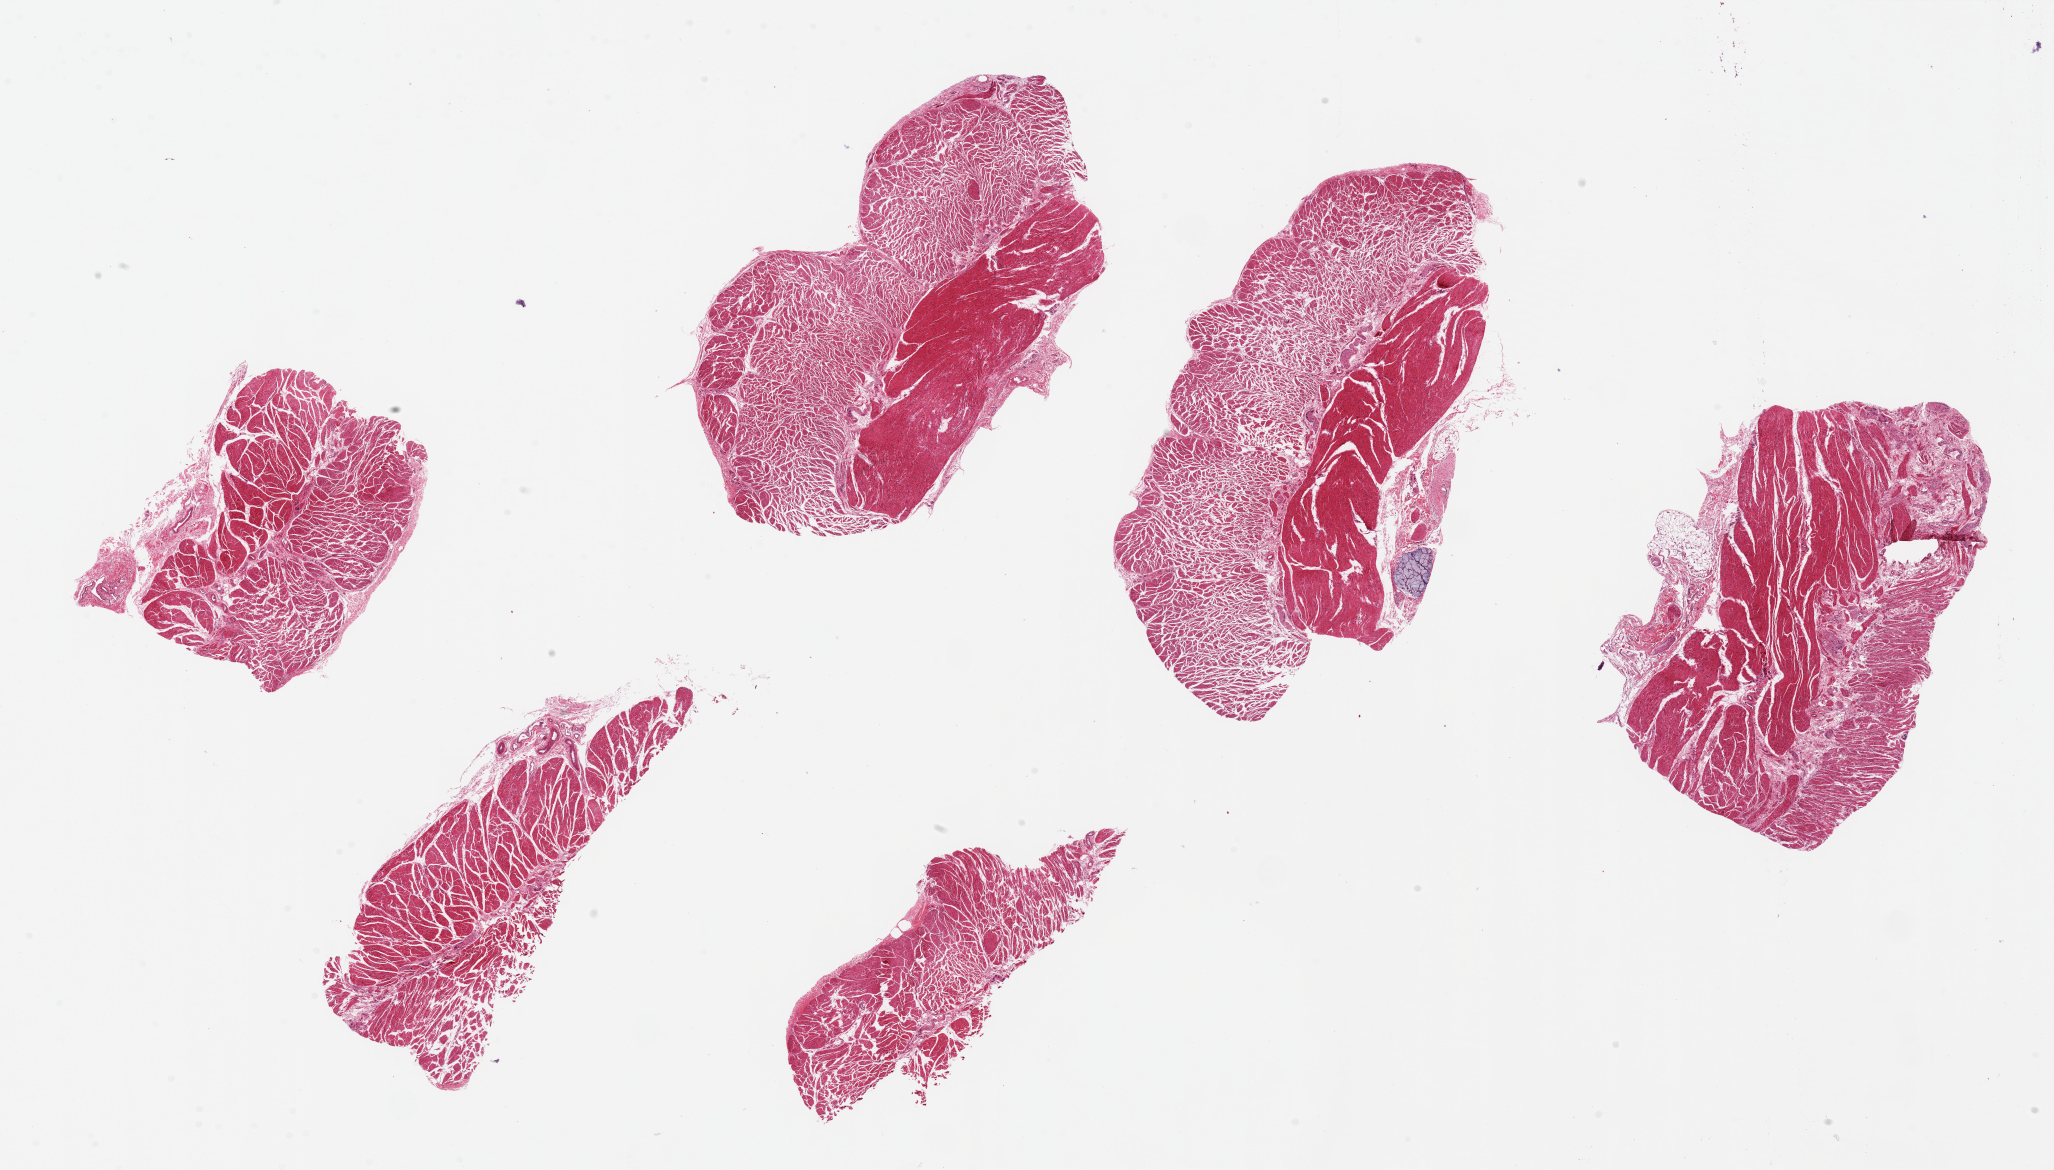
Hematoxylin and eosin (H&E) whole-slide image — low-resolution overview of the scanned area, about 32.5 x 18.5 mm (acquisition: 20x scan). PAXgene-fixed paraffin-embedded (PFPE) section. Section of esophageal muscle (target tissue). Donor tissue sample.
* pathologist's review note for this sample: 6 pieces ~8x4mm, rare submucosal glands noted